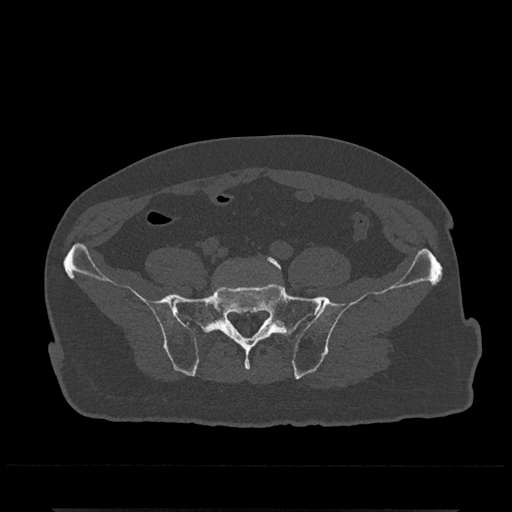
CT including the spine, one axial slice. Position 35 of 797 along the scan axis. Reconstruction kernel Br40s/3. 120 kVp. Bone window (W 1800 / L 400 HU). 0.5 mm slice thickness. 512 × 512 image matrix, field of view 393 × 393 mm. Patient: male, 67 years. From the clinical record (not read from this slice): primary cancer: prostate.
Annotated regions visible in this slice (semi-automatically segmented with operator editing):
- L5 vertebra: box from (x=224, y=257) to (x=281, y=270) px